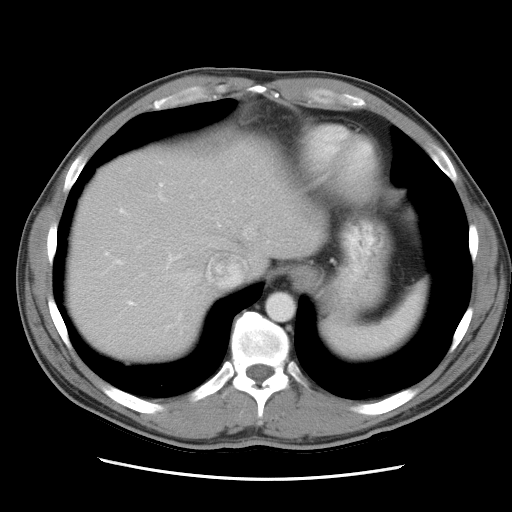
Contrast-enhanced abdominal CT, one axial slice; slice 25 of 34 in the series (ordered by position); reconstruction kernel STANDARD; 120 kVp; soft-tissue window (W 400 / L 40 HU); 7.5 mm slice thickness; 512 × 512 image matrix, field of view 360 × 360 mm. Male patient, age 40 years. Case-level facts recorded for this patient, not image findings: diagnosis: colorectal cancer liver metastases, imaged before liver resection; multiple liver metastases: yes; largest metastasis: 1.5 cm; disease in both lobes: yes.
Annotated regions visible in this slice (outlined manually by an expert reader):
- hepatic veins: bounding box (x1, y1, x2, y2) in pixels: (164, 227, 252, 290)
- liver: (67, 132, 320, 358)
- planned liver remnant (the part of the liver to remain after resection): (67, 131, 318, 358)
- portal vein (with intrahepatic branches): (116, 184, 182, 321)